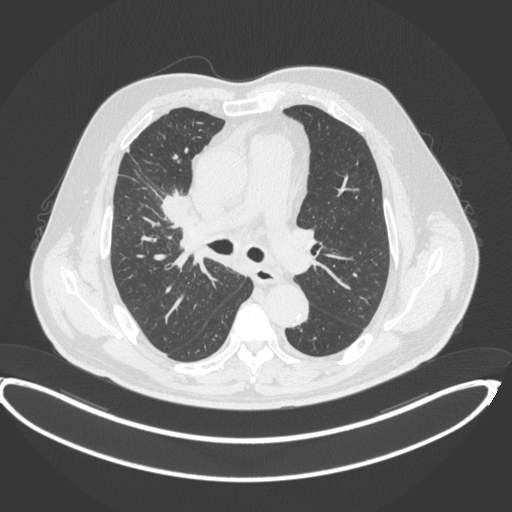
Chest CT, one axial slice; position 256 of 395 along the scan axis; reconstruction kernel B31f; lung window (W 1500 / L -600 HU); 512 × 512 image matrix, field of view 448 × 448 mm. Patient: male, 62 years. From the clinical record (not read from this slice): clinical TNM (as recorded): T1c N3 M1c.
Annotated regions visible in this slice (bounding box drawn by a radiologist):
- lung tumour (recorded histology: adenocarcinoma): bounding box (x1, y1, x2, y2) in pixels: (160, 189, 192, 226)